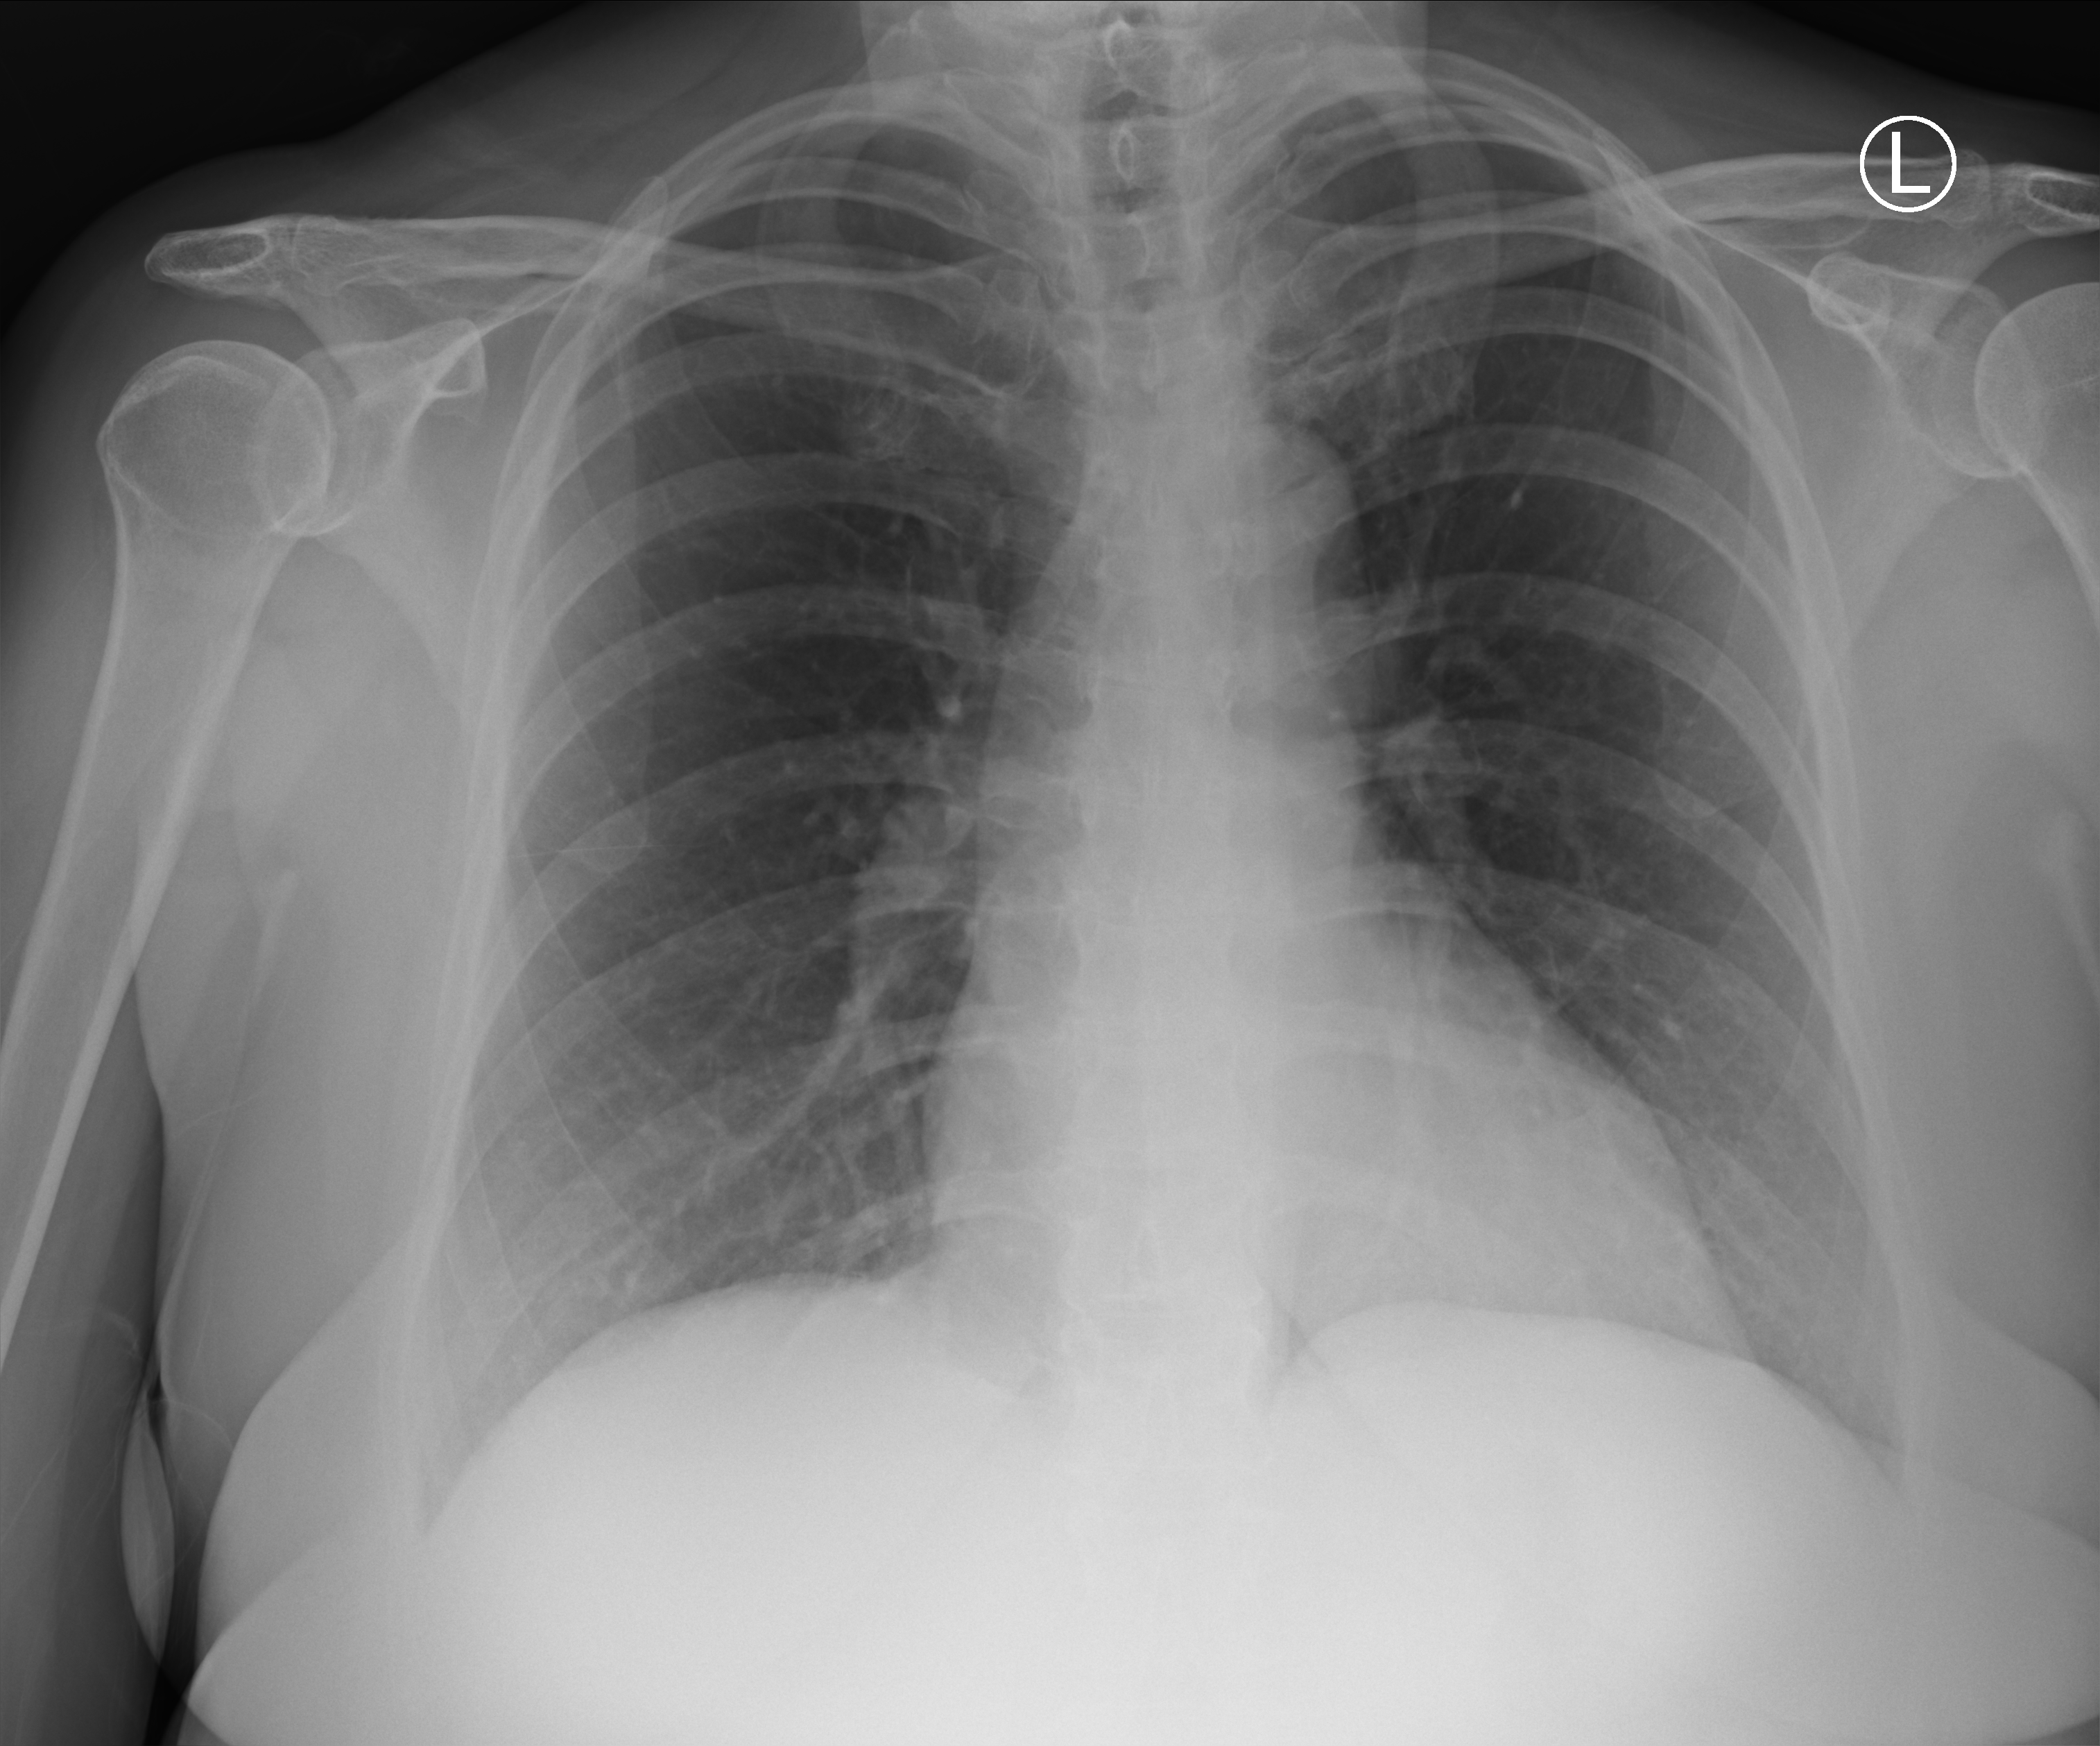
Chest X-ray (portable). Patient hospitalised with COVID-19; female, aged 18–59 years.
From the hospital-stay record, not from the radiograph (when in the stay this image was taken is not recorded): admitted to intensive care during this hospital stay: yes; other chronic lung disease (admission record): yes.